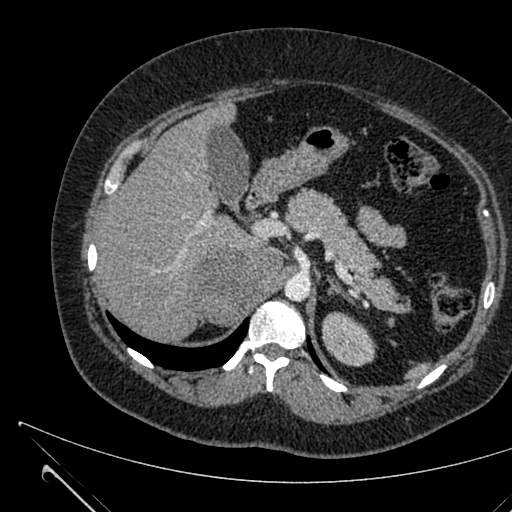
Contrast-enhanced abdominal CT, one axial slice; soft-tissue window (W 400 / L 40 HU); 1 mm slice thickness; 512 × 512 image matrix, field of view 376 × 376 mm. Female patient, age 36 years. From the clinical record (not read from this slice): diagnosis: adrenocortical carcinoma; tumour side: right adrenal; tumour size at pathology: 10 cm; Ki-67 index: 20 %; stage (as recorded): 4.
Outlined on this slice (semi-automatic segmentation, software-assisted and operator-edited):
- mass: bounding box <193,250,285,324> (left, top, right, bottom; pixels)